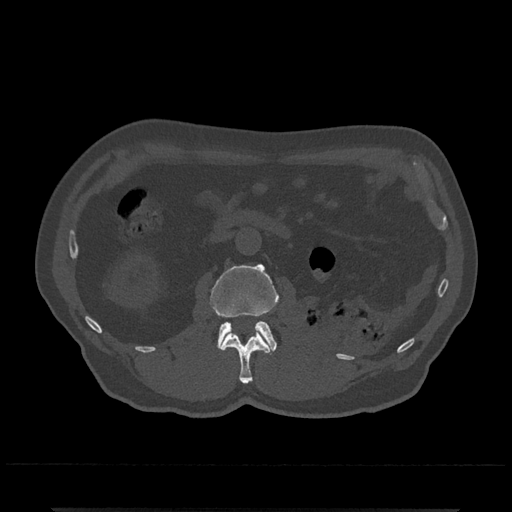
CT including the spine, one axial slice. Slice 321 of 797 in the series (ordered by position). Reconstruction kernel Br40s/3. 120 kVp. Bone window (W 1800 / L 400 HU). 0.5 mm slice thickness. 512 × 512 image matrix, field of view 393 × 393 mm. Patient: male, 67 years. Case-level facts recorded for this patient, not image findings: primary cancer: prostate.
Outlined on this slice (semi-automatically segmented with operator editing):
- L1 vertebra: bounding box [x1, y1, x2, y2] px = [219, 331, 270, 384]
- L2 vertebra: [210, 264, 278, 353]